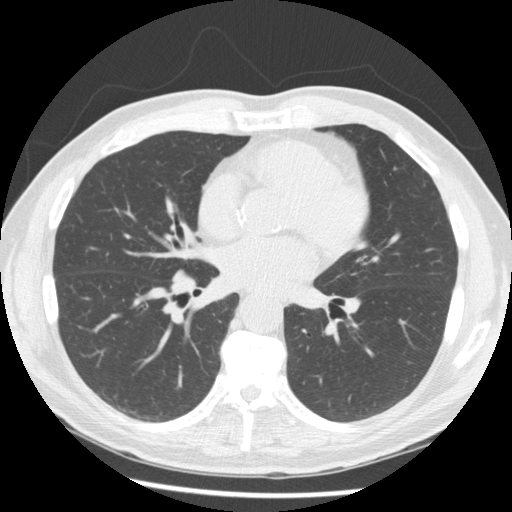
Axial slice from a low-dose chest CT screening exam. Baseline screening round. Lung window (W 1500 / L -600 HU). Slice 84 of 166 in the series. 512 × 512 image matrix. Male participant, aged 62 years at enrolment. Current smoker at enrolment.
Lesion marked by an expert reader, bounding box [x1, y1, x2, y2] px = [152, 255, 214, 312]. Screening reader's record for this exam: no non-calcified nodule ≥4 mm recorded. Participant outcome: lung cancer diagnosed 146 days after this screen — small cell carcinoma, NOS, right hilum, mediastinum, poorly differentiated (G3), stage IV (AJCC 6th edition).